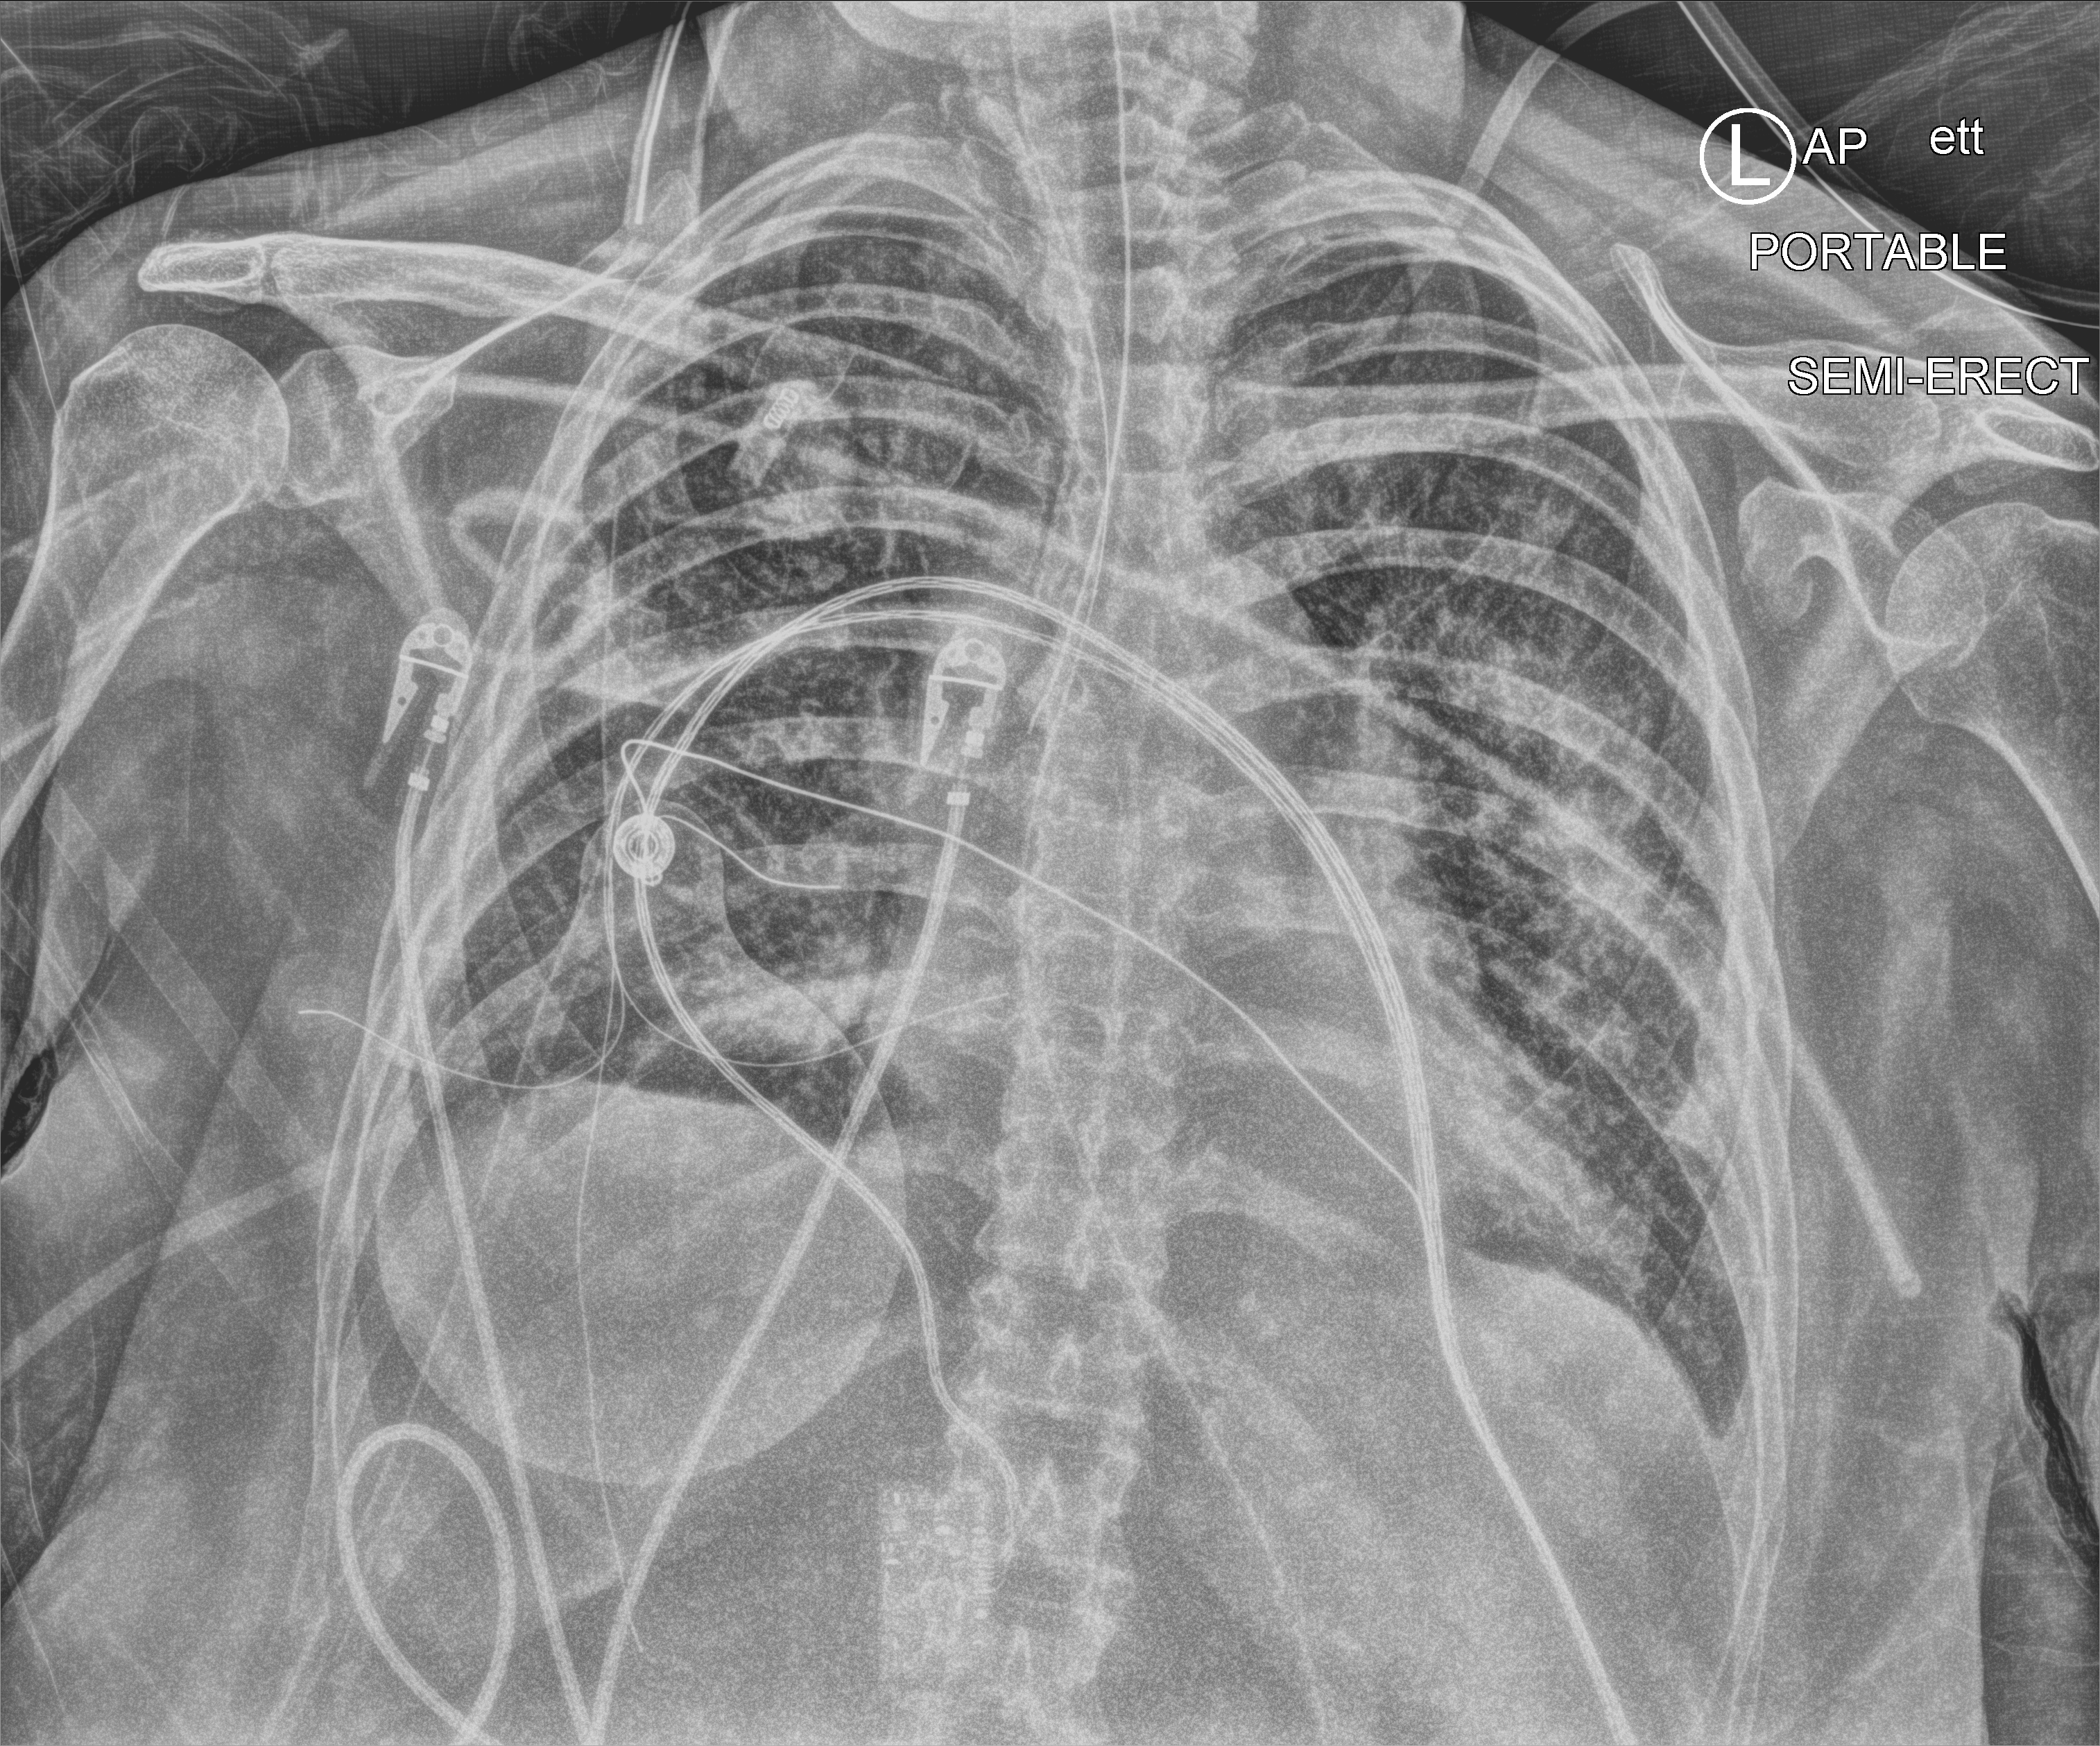
Chest X-ray (portable), anteroposterior (AP) projection. Female patient hospitalised with COVID-19, age 60–74 years.
From the hospital-stay record, not from the radiograph (when in the stay this image was taken is not recorded): mechanically ventilated during this hospital stay: yes.